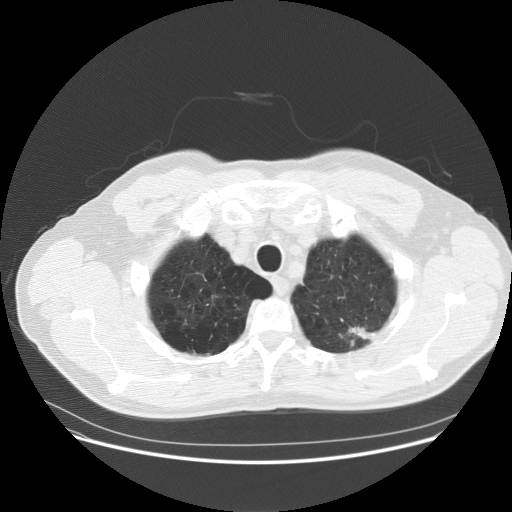
Chest CT (low-dose screening protocol), one axial image; baseline screening round; lung window (W 1500 / L -600 HU); 2.5 mm slice thickness; standard (soft-tissue) reconstruction kernel (STANDARD); slice 15 of 158 in the series. Male participant, aged 61 years at enrolment.
• Expert reader's lesion annotation, box from (x=328, y=310) to (x=393, y=365) px.
• Reader record for this screening exam (exam-level; its link to the box is not recorded): non-calcified nodule or mass ≥4 mm, left upper lobe, 12 × 6 mm, poorly defined margins, soft tissue attenuation.